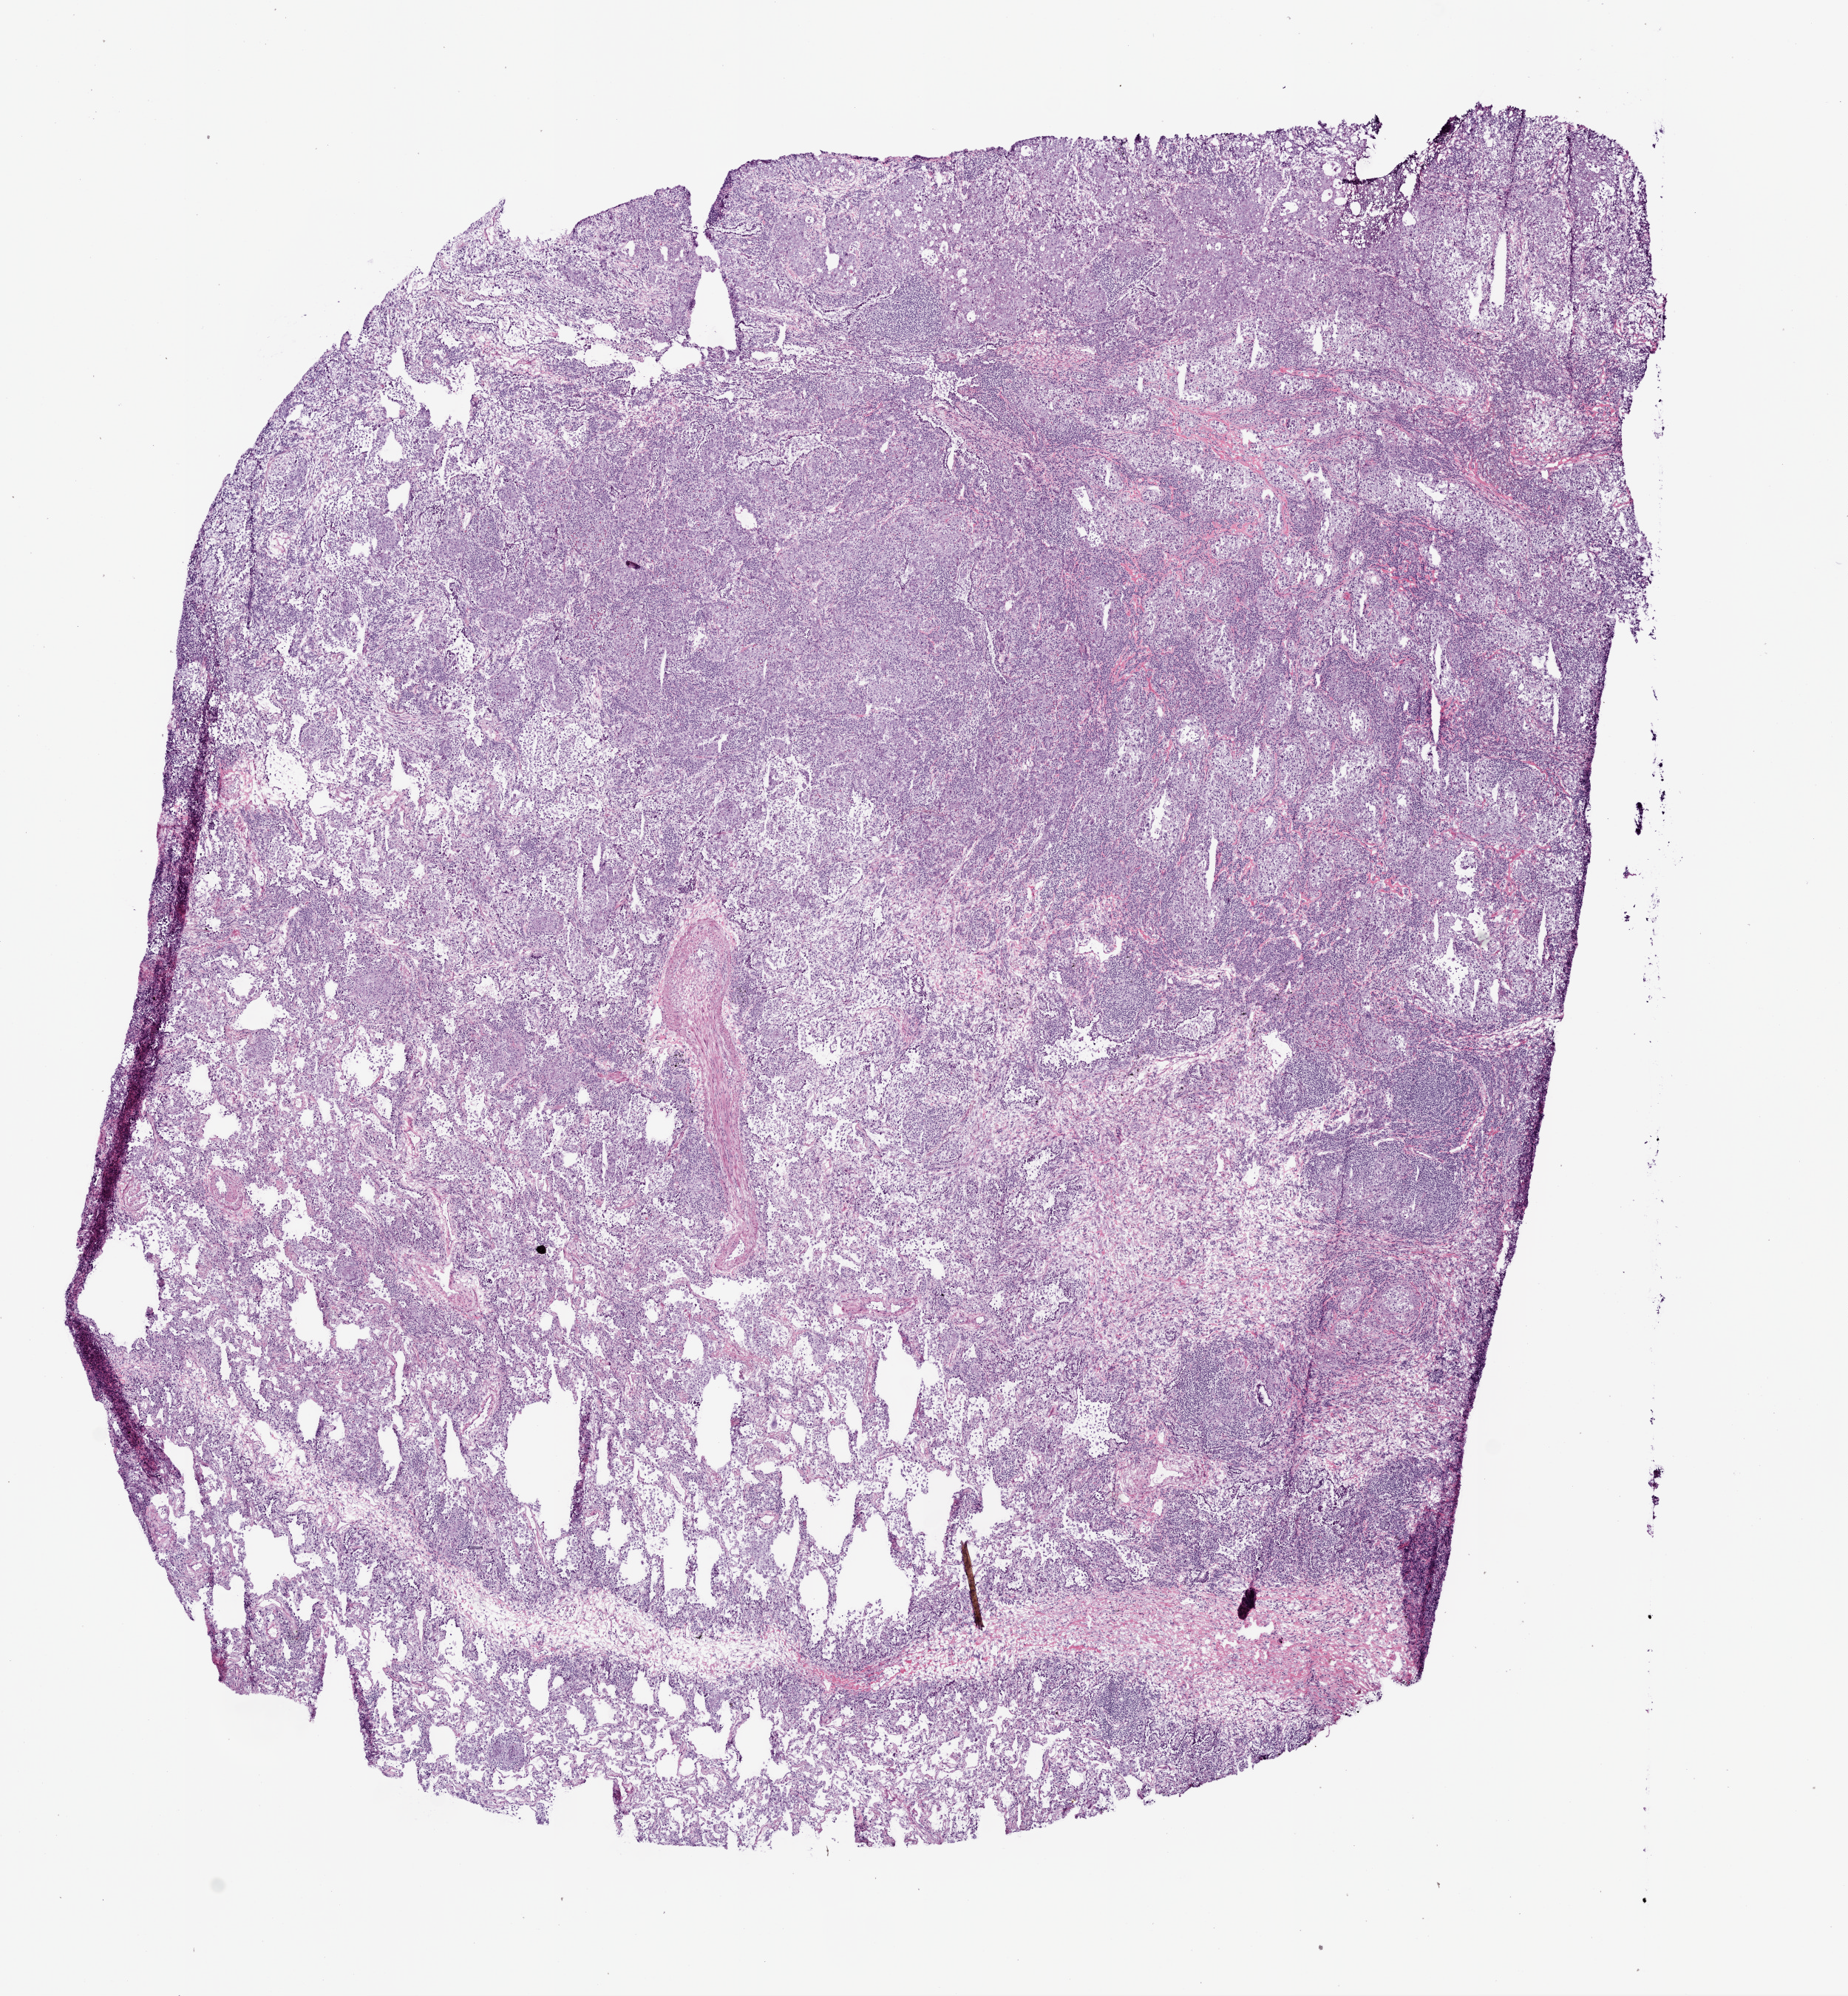
Whole-slide histology image, H&E-stained — whole scanned area (about 10.0 x 10.8 mm) shown as a low-resolution overview; frozen section from the bottom of the tissue portion; lung, primary tumour sample. Male, age 67 years at initial diagnosis. Composition of this section per pathologist review: tumour cells 50%, tumour nuclei 40%, normal cells 50%, stromal cells 0%, necrosis 0%. Infiltration values recorded for this section: lymphocyte infiltration 40%, monocyte infiltration 10%, neutrophil infiltration 0%.
AJCC pathologic stage: IIIA (6th edition). Diagnosis: Adenocarcinoma, NOS.